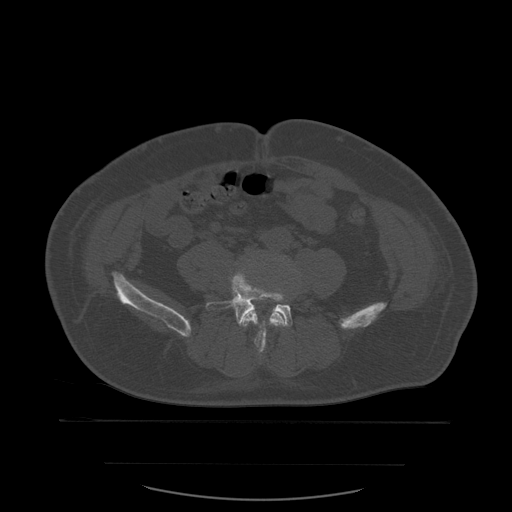
CT including the spine, one axial slice; slice 149 of 590 in the series (ordered by position); bone window (W 1800 / L 400 HU); 1.25 mm slice thickness; 512 × 512 image matrix, field of view 479 × 479 mm. Patient age 71 years. Case-level facts recorded for this patient, not image findings: primary cancer: lung; vertebrae with lytic lesions (as recorded): T1, T2, L5, S1.
Outlined on this slice (semi-automatic segmentation, software-assisted and operator-edited):
- L4 vertebra: box from (x=243, y=310) to (x=286, y=349) px
- L5 vertebra: (x=206, y=269)–(x=293, y=352)